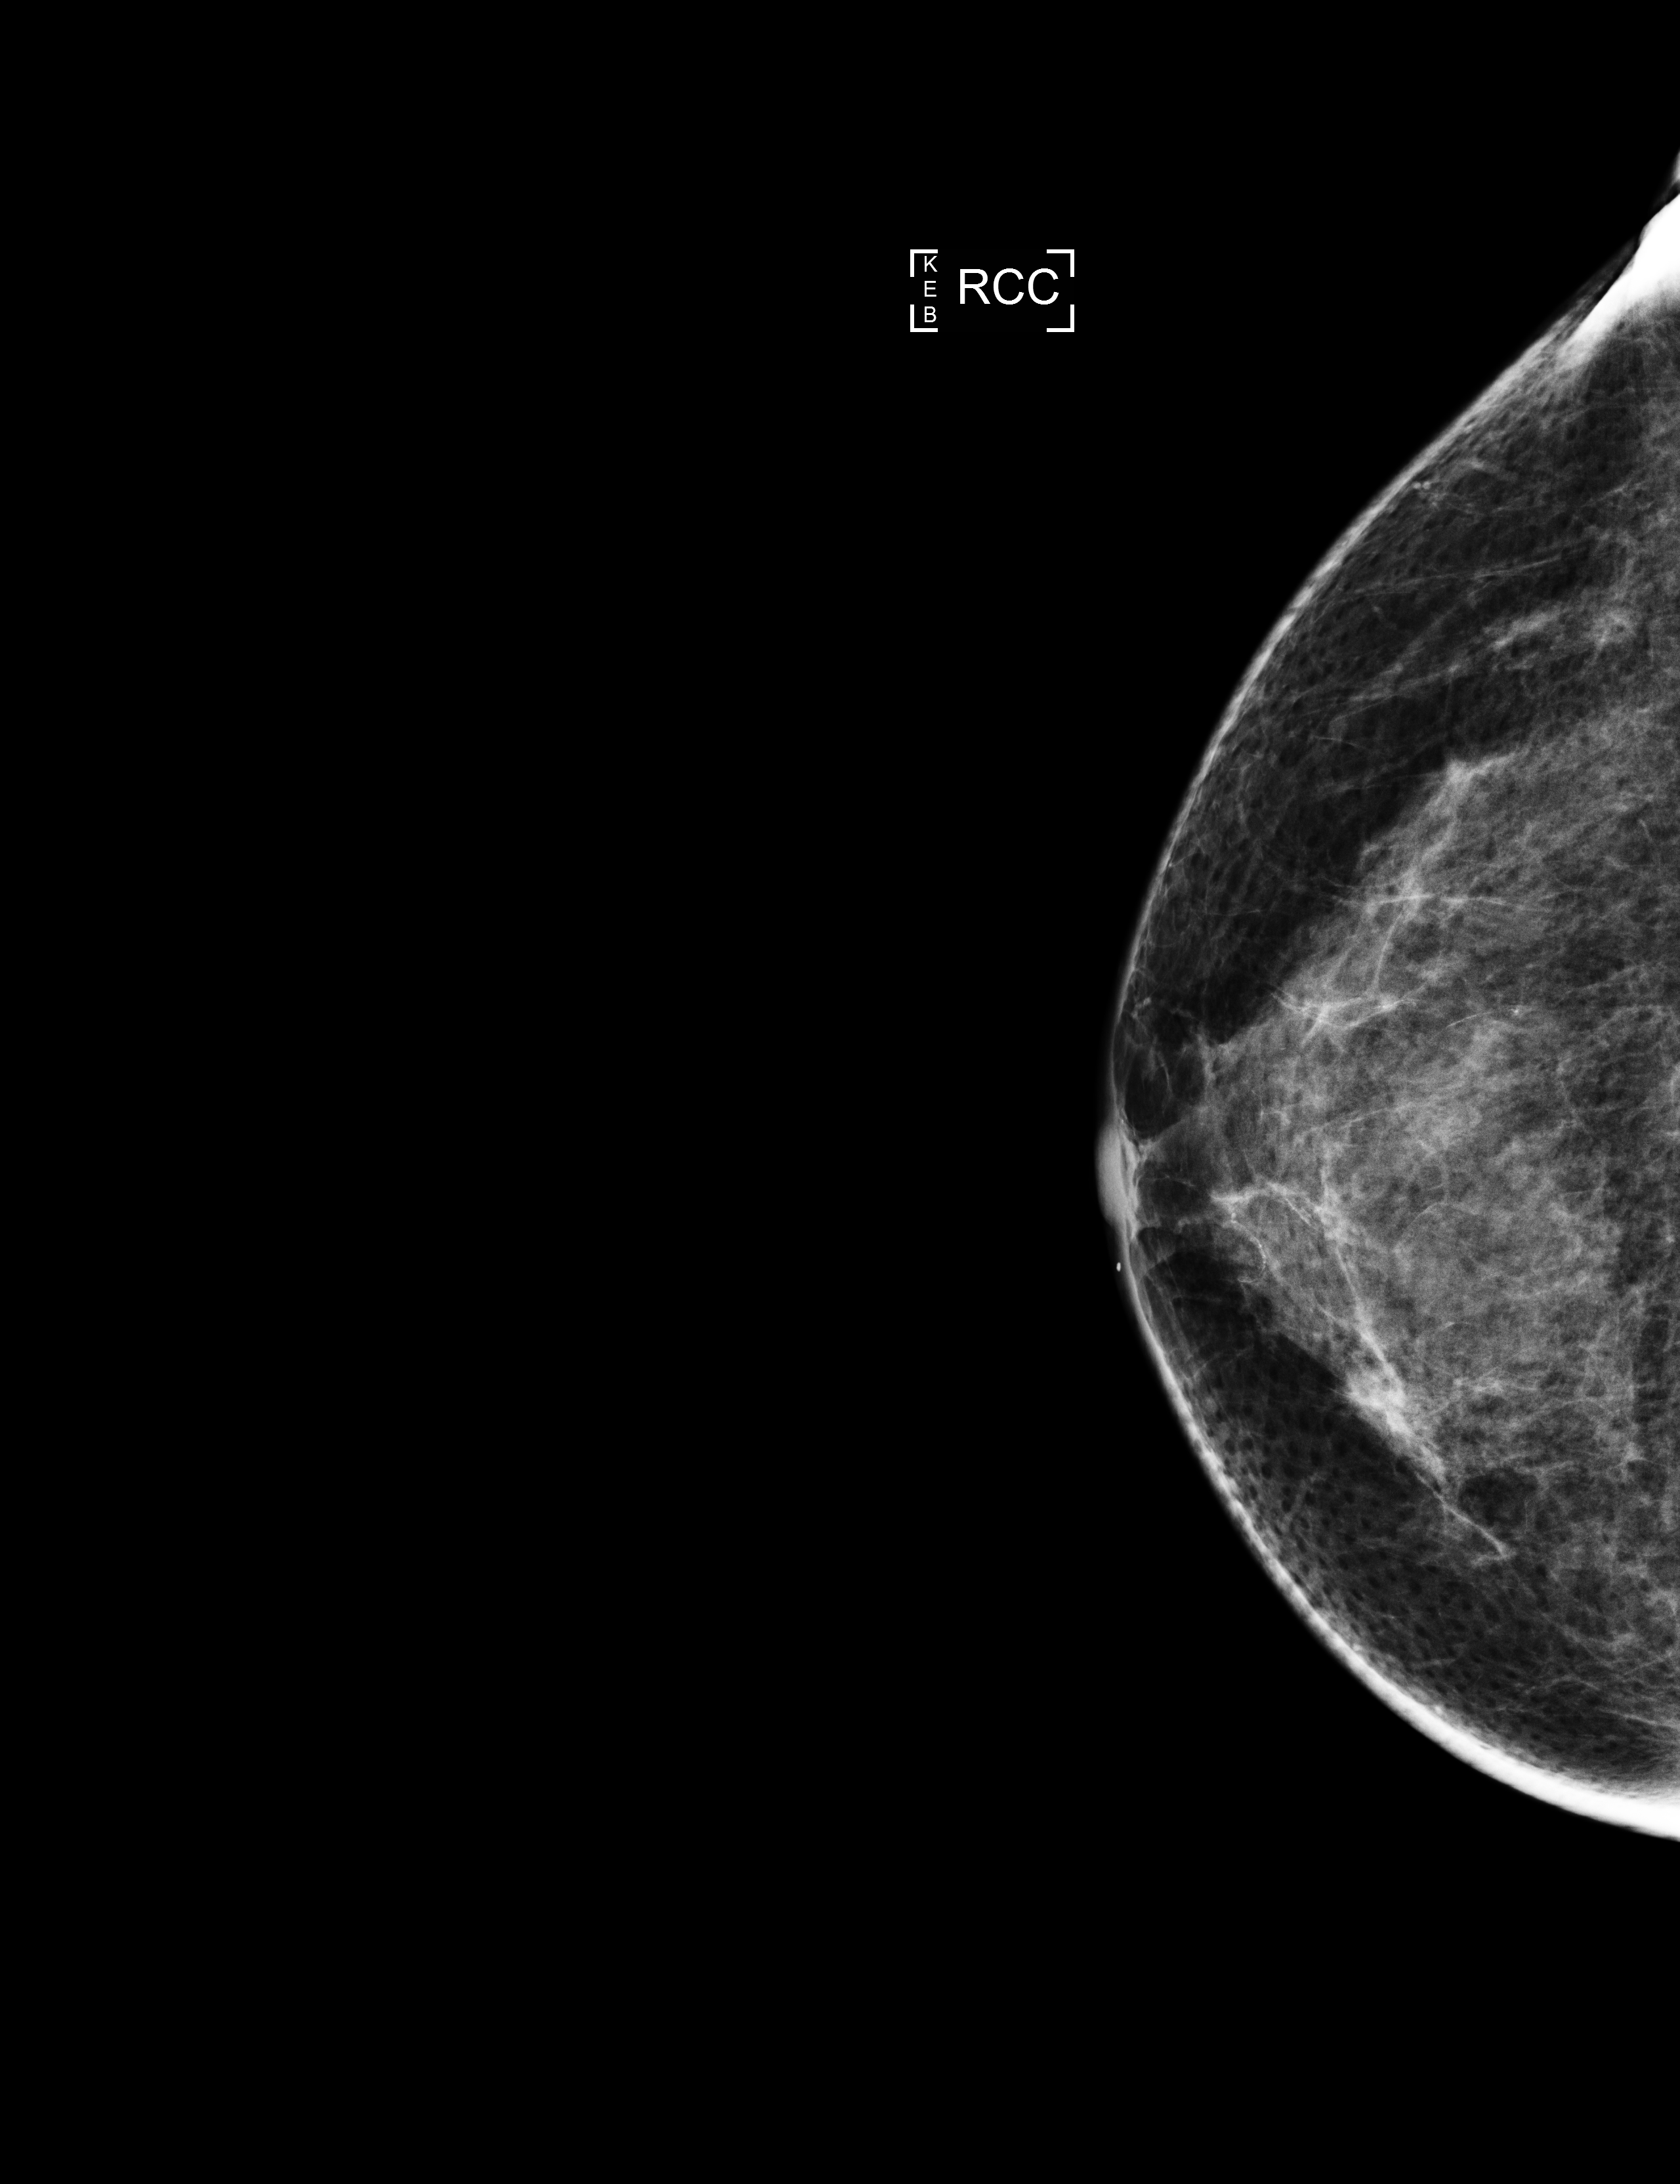
Screening examination. Patient aged 65 years (female).
Image type: full-field digital mammogram. Breast: right. Projection: craniocaudal (CC) view.